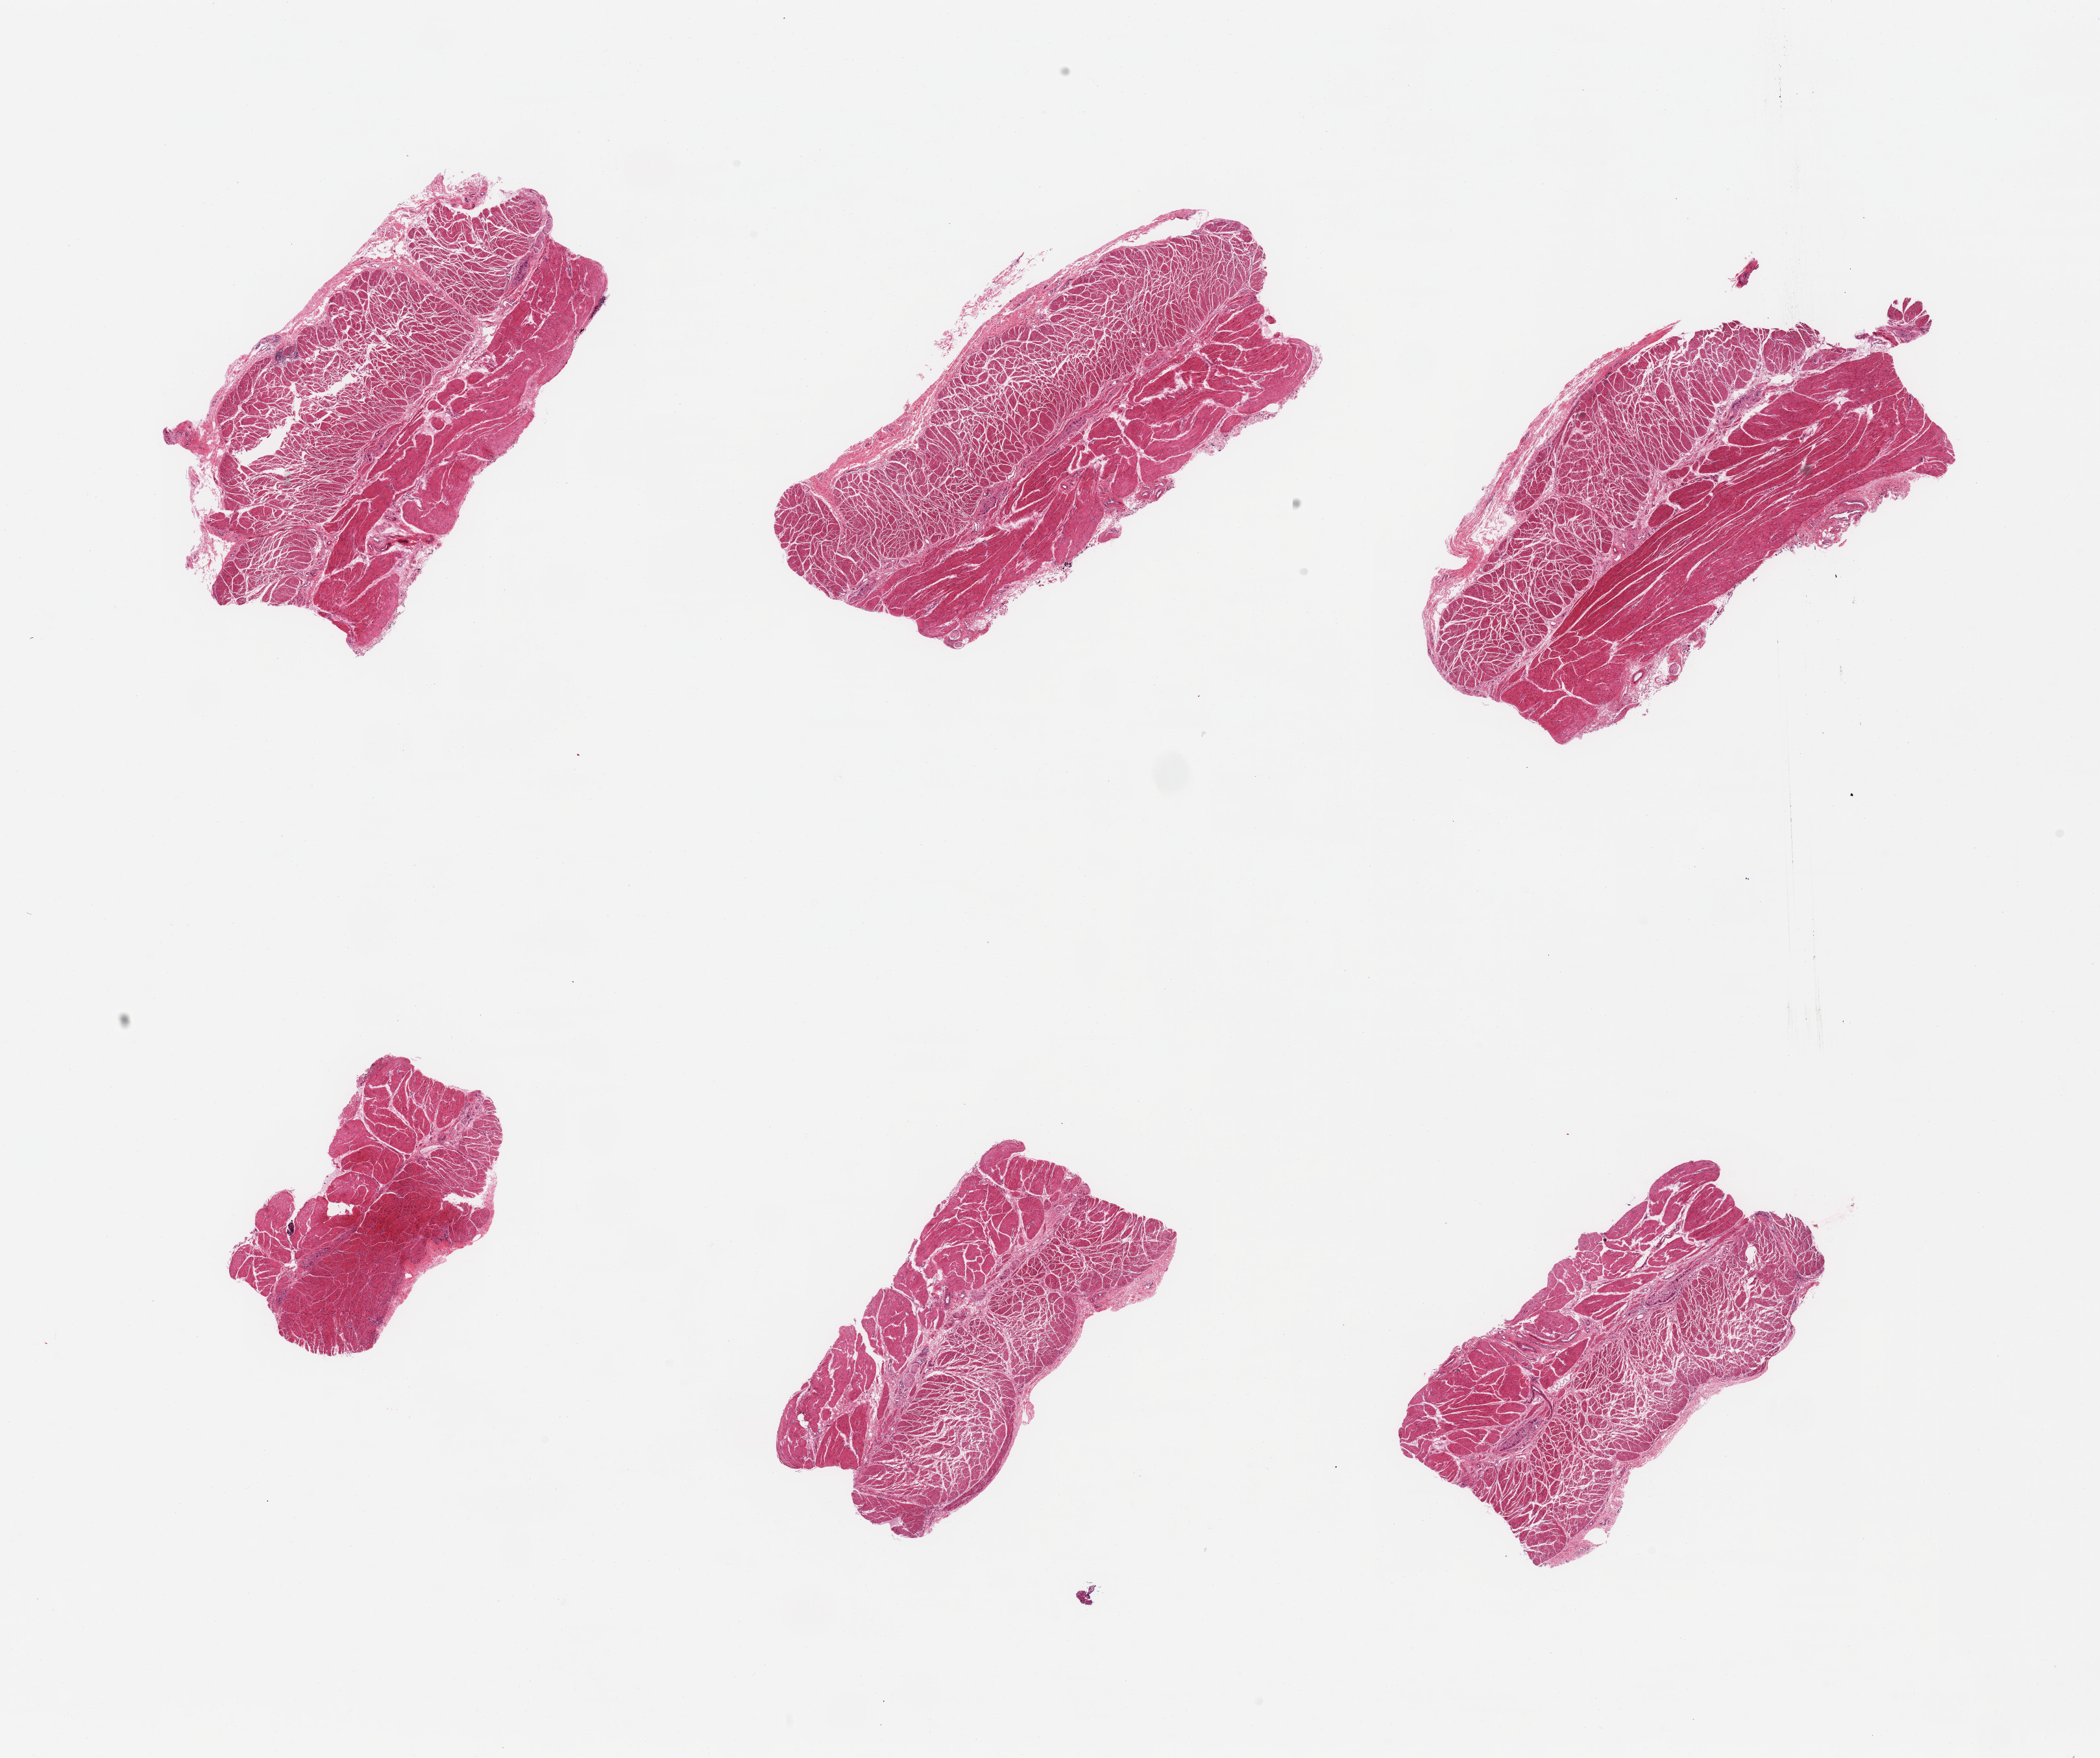
Digitized haematoxylin and eosin-stained section — whole scanned area (about 25.6 x 21.4 mm, slide scanned at 20x) shown as a low-resolution overview. PAXgene-fixed, paraffin-embedded tissue. Section of esophageal muscle (target tissue). Donor tissue sample. Donor: male.
Pathologist's review note for this sample: 6 pieces; well trimmed target muscularis.